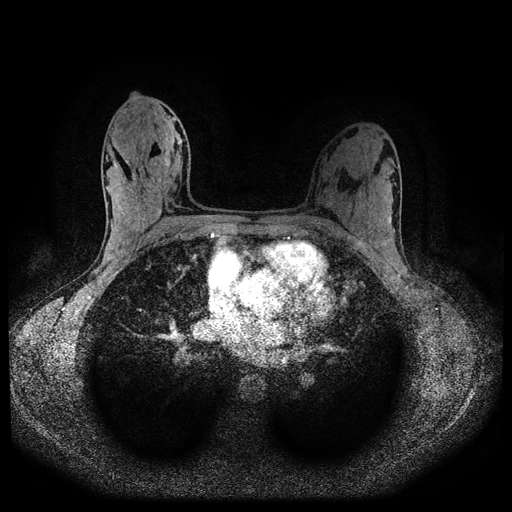
Breast MRI (dynamic contrast-enhanced, multi-phase), one axial slice; slice 60 of 116 in the series (ordered by position); dynamic contrast-enhanced series, time point 2 of 5 at this slice position (early post-contrast); 1.5 T; TE 2.7 ms, TR 5.4 ms; 2 mm slice thickness; 512 × 512 image matrix, field of view 330 × 330 mm. Patient: female, 32 years.
Outlined on this slice (semi-automatic segmentation, software-assisted and operator-edited):
- breast lesion (labelled benign in the annotation): bounding box <111,160,120,179> (left, top, right, bottom; pixels)